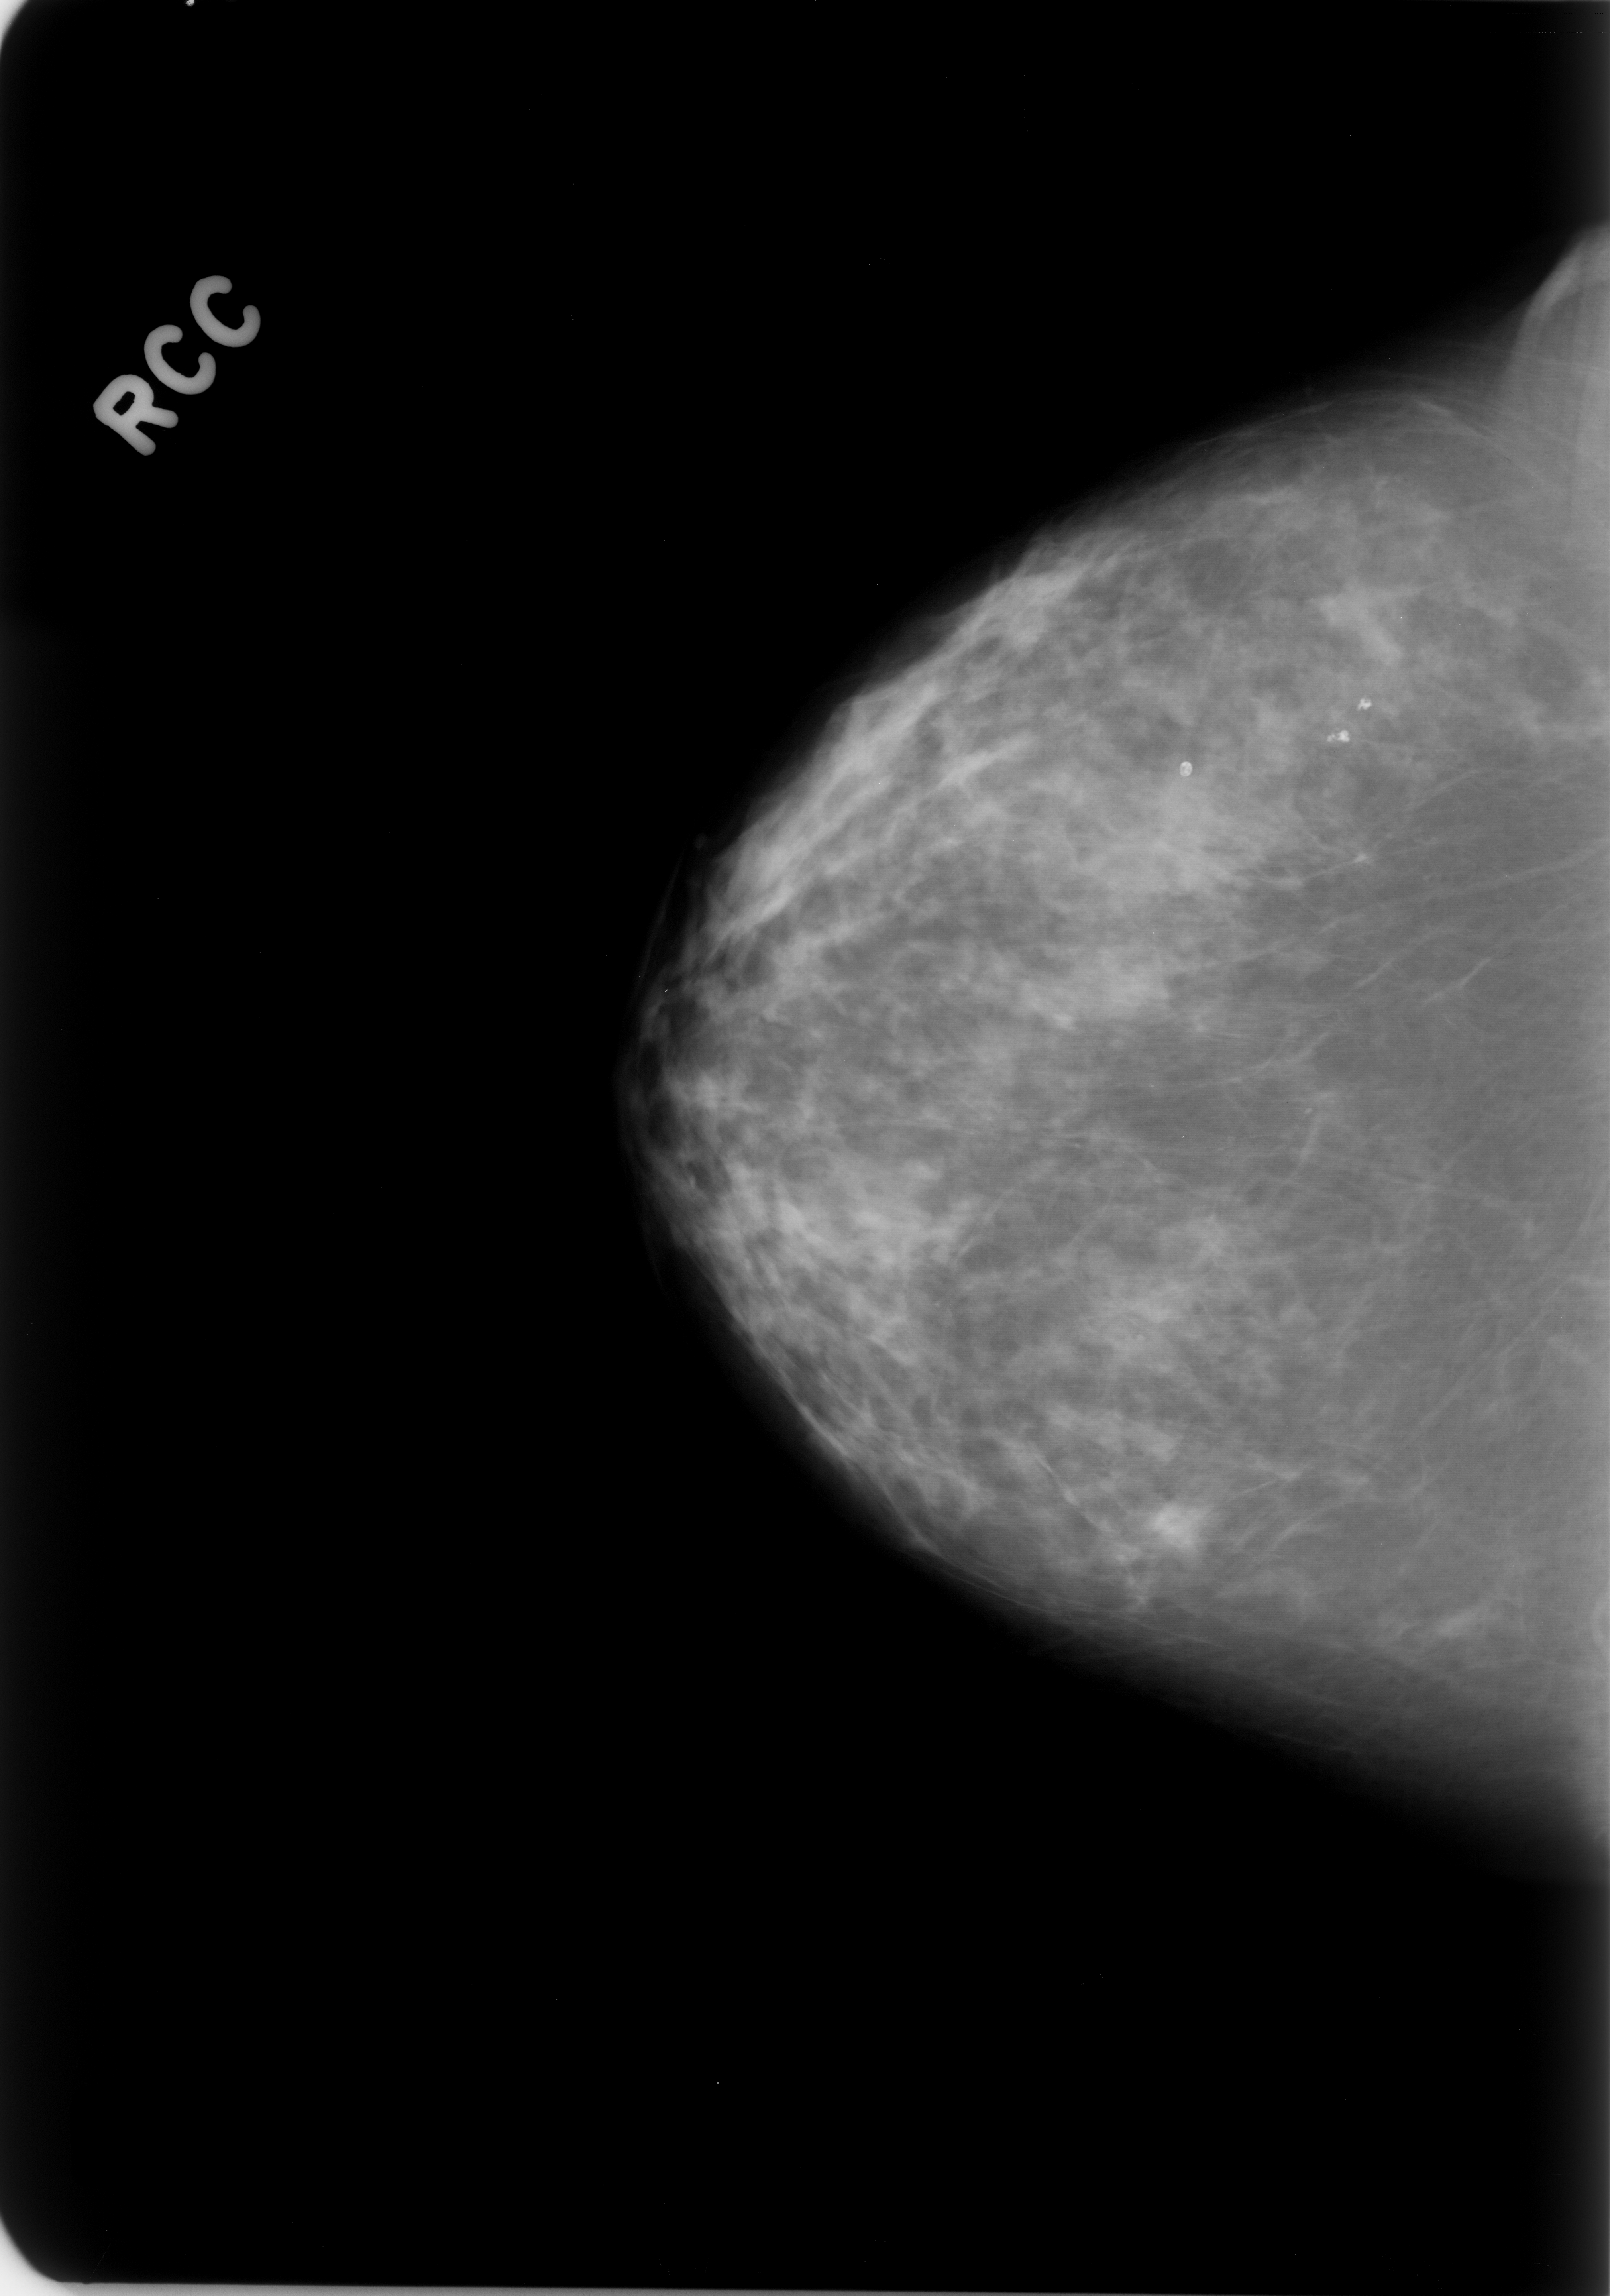
Digitized screen-film mammogram; right breast; CC view; 1610 × 2296 image matrix.
Marked abnormalities (boxes around the expert regions of interest):
- calcifications, morphology fine linear branching, distribution linear; BI-RADS assessment category 4; subtlety rating 2 on a 1 (subtle) to 5 (obvious) scale; pathology (as recorded): benign: bounding box [x1, y1, x2, y2] px = [1176, 1074, 1362, 1187]